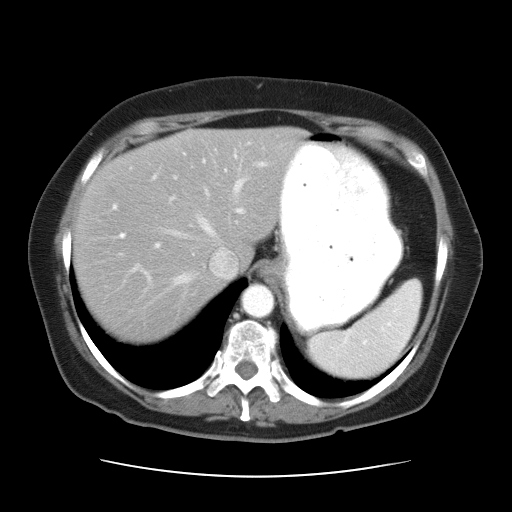
Contrast-enhanced abdominal CT, one axial slice. Position 26 of 34 along the scan axis. Reconstruction kernel STANDARD. 120 kVp. Intravenous contrast given. Soft-tissue window (W 400 / L 40 HU). 7.5 mm slice thickness. 512 × 512 image matrix, field of view 360 × 360 mm. Female patient, age 65 years. From the clinical record (not read from this slice): diagnosis: colorectal cancer liver metastases, imaged before liver resection; multiple liver metastases: yes; largest metastasis: 2.2 cm; disease in both lobes: no.
Structures marked on this image (manually delineated by an expert):
- hepatic veins: box from (x=111, y=161) to (x=266, y=286) px
- liver: (x=77, y=129)–(x=298, y=338)
- planned liver remnant (the part of the liver to remain after resection): (x=77, y=129)–(x=297, y=333)
- portal vein (with intrahepatic branches): (x=121, y=149)–(x=245, y=247)
- liver metastasis: (x=104, y=187)–(x=120, y=199)